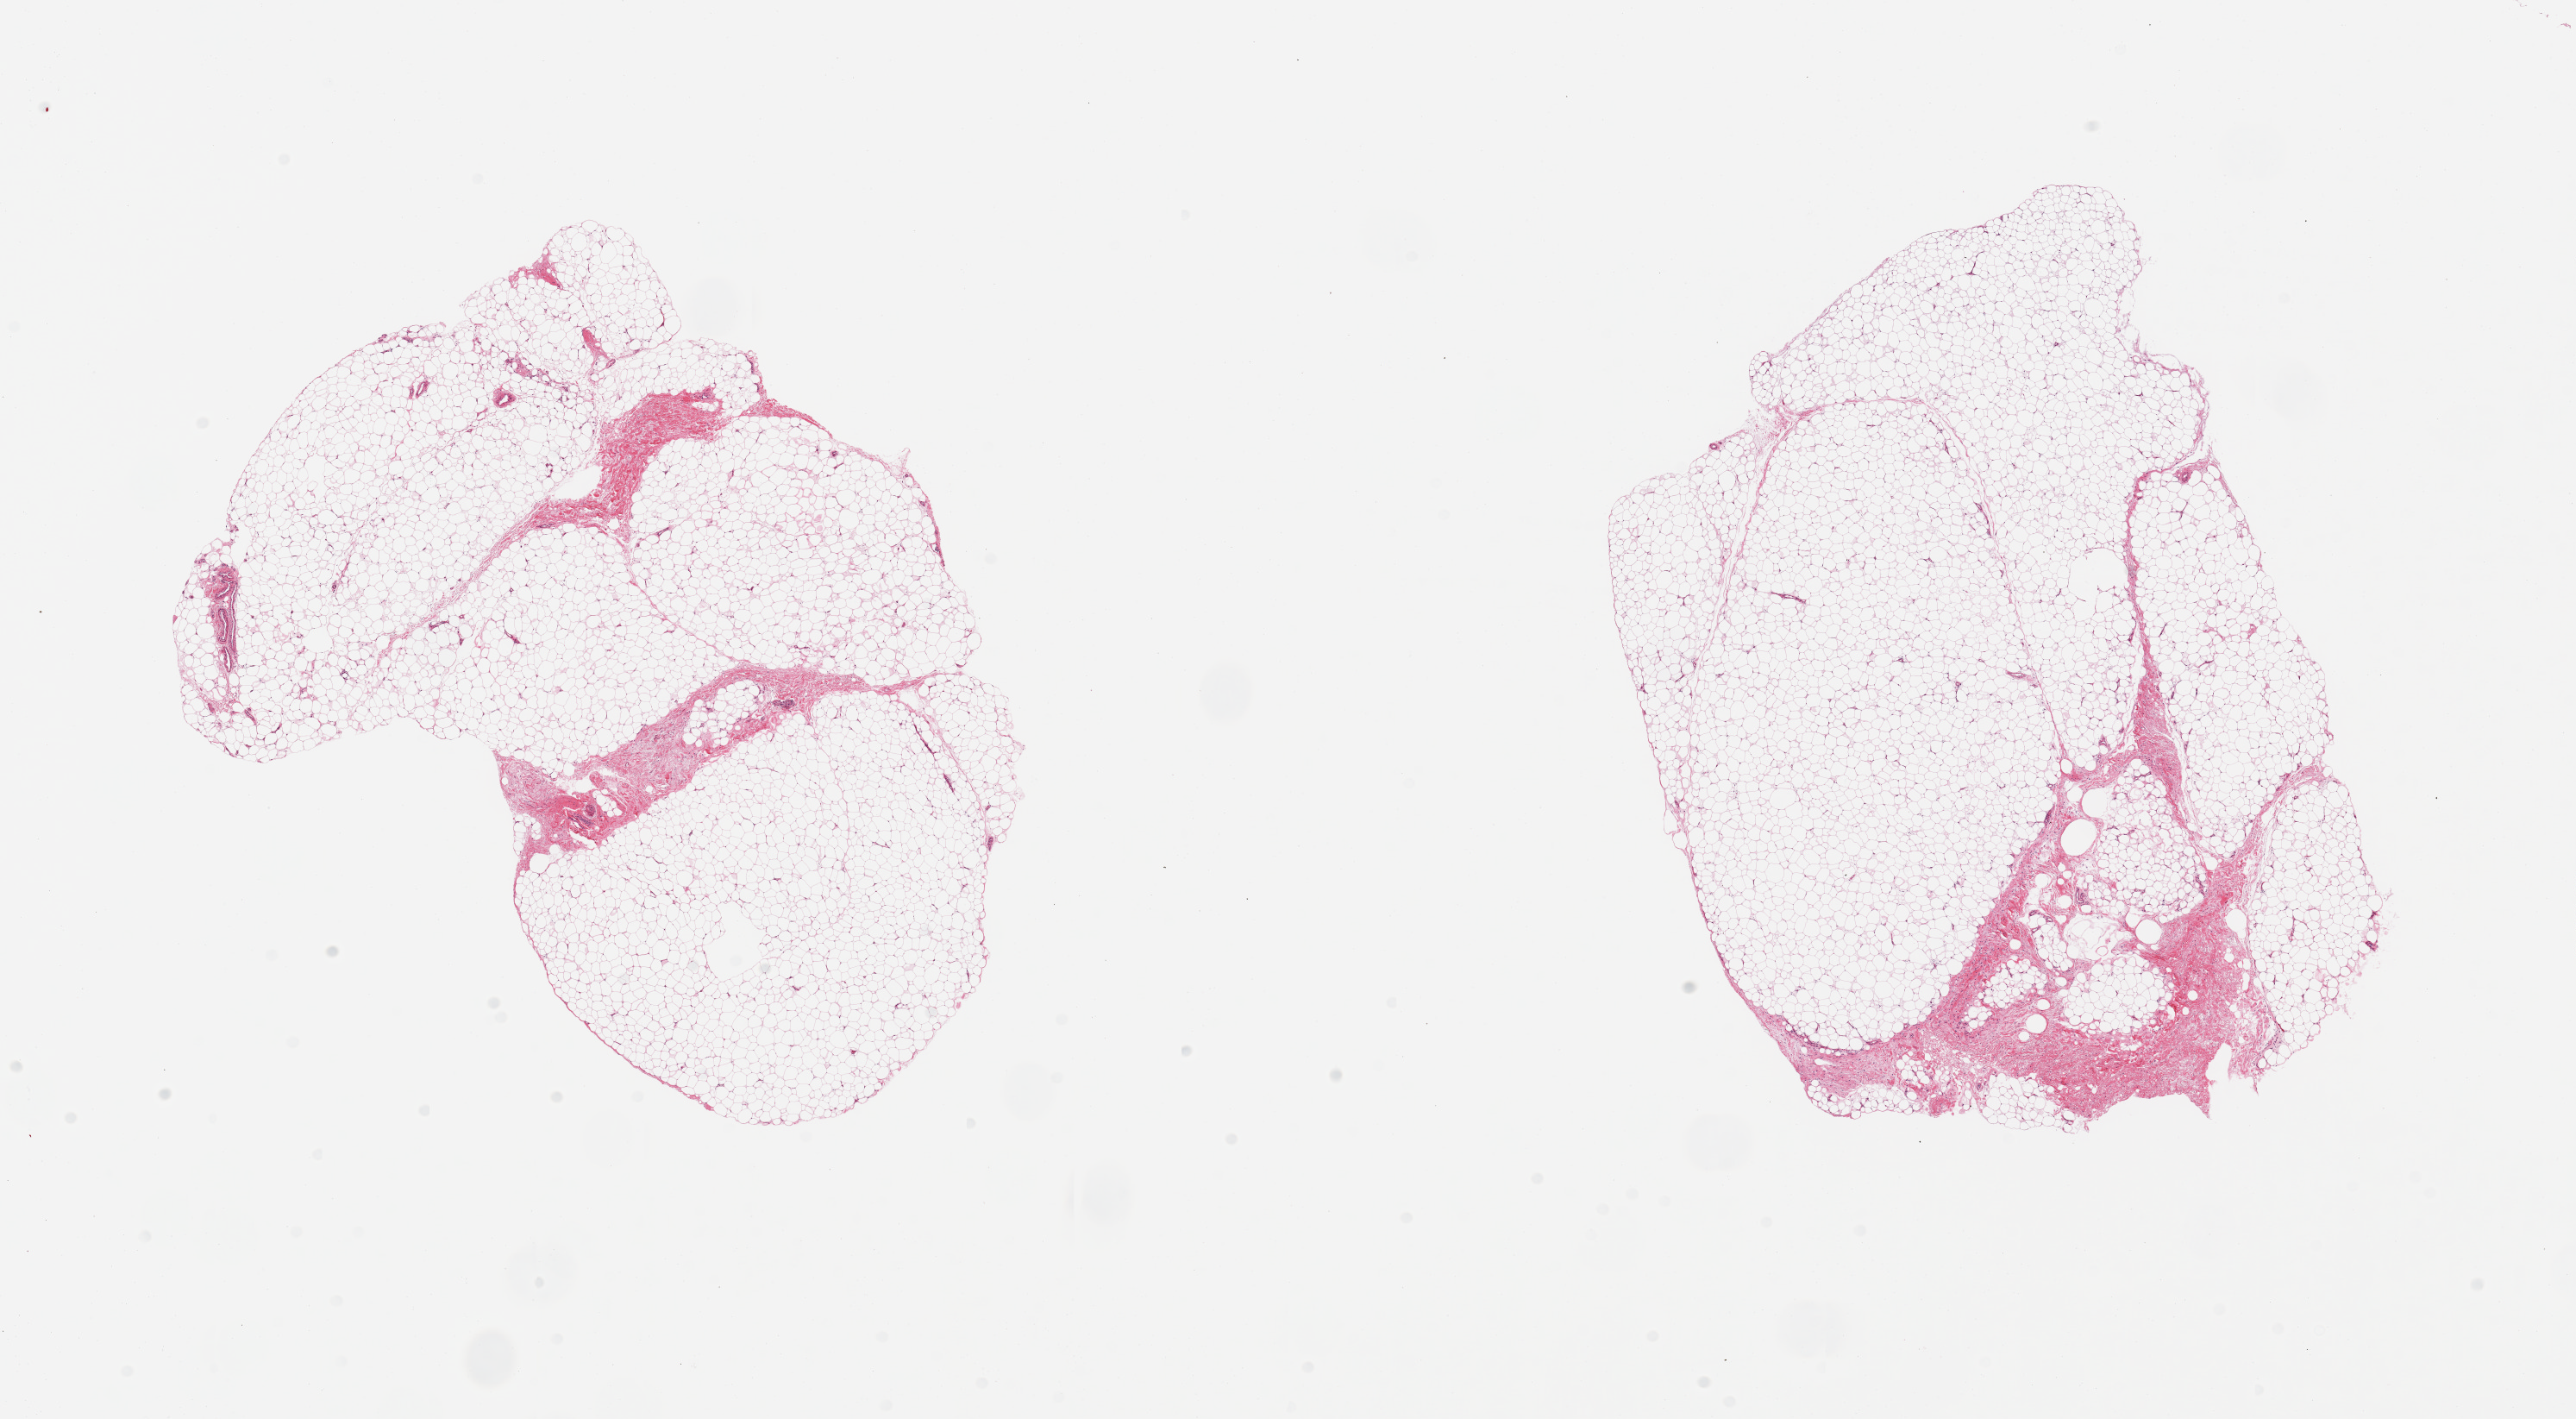
Whole-slide image, hematoxylin and eosin (H&E) stain — whole scanned area (about 23.6 x 13.0 mm) shown as a low-resolution overview; PAXgene-fixed paraffin-embedded (PFPE) section; section of adipose tissue (target tissue); donor tissue sample.
Reviewer comment on this tissue sample: 2 pieces; 5% fibrous content.